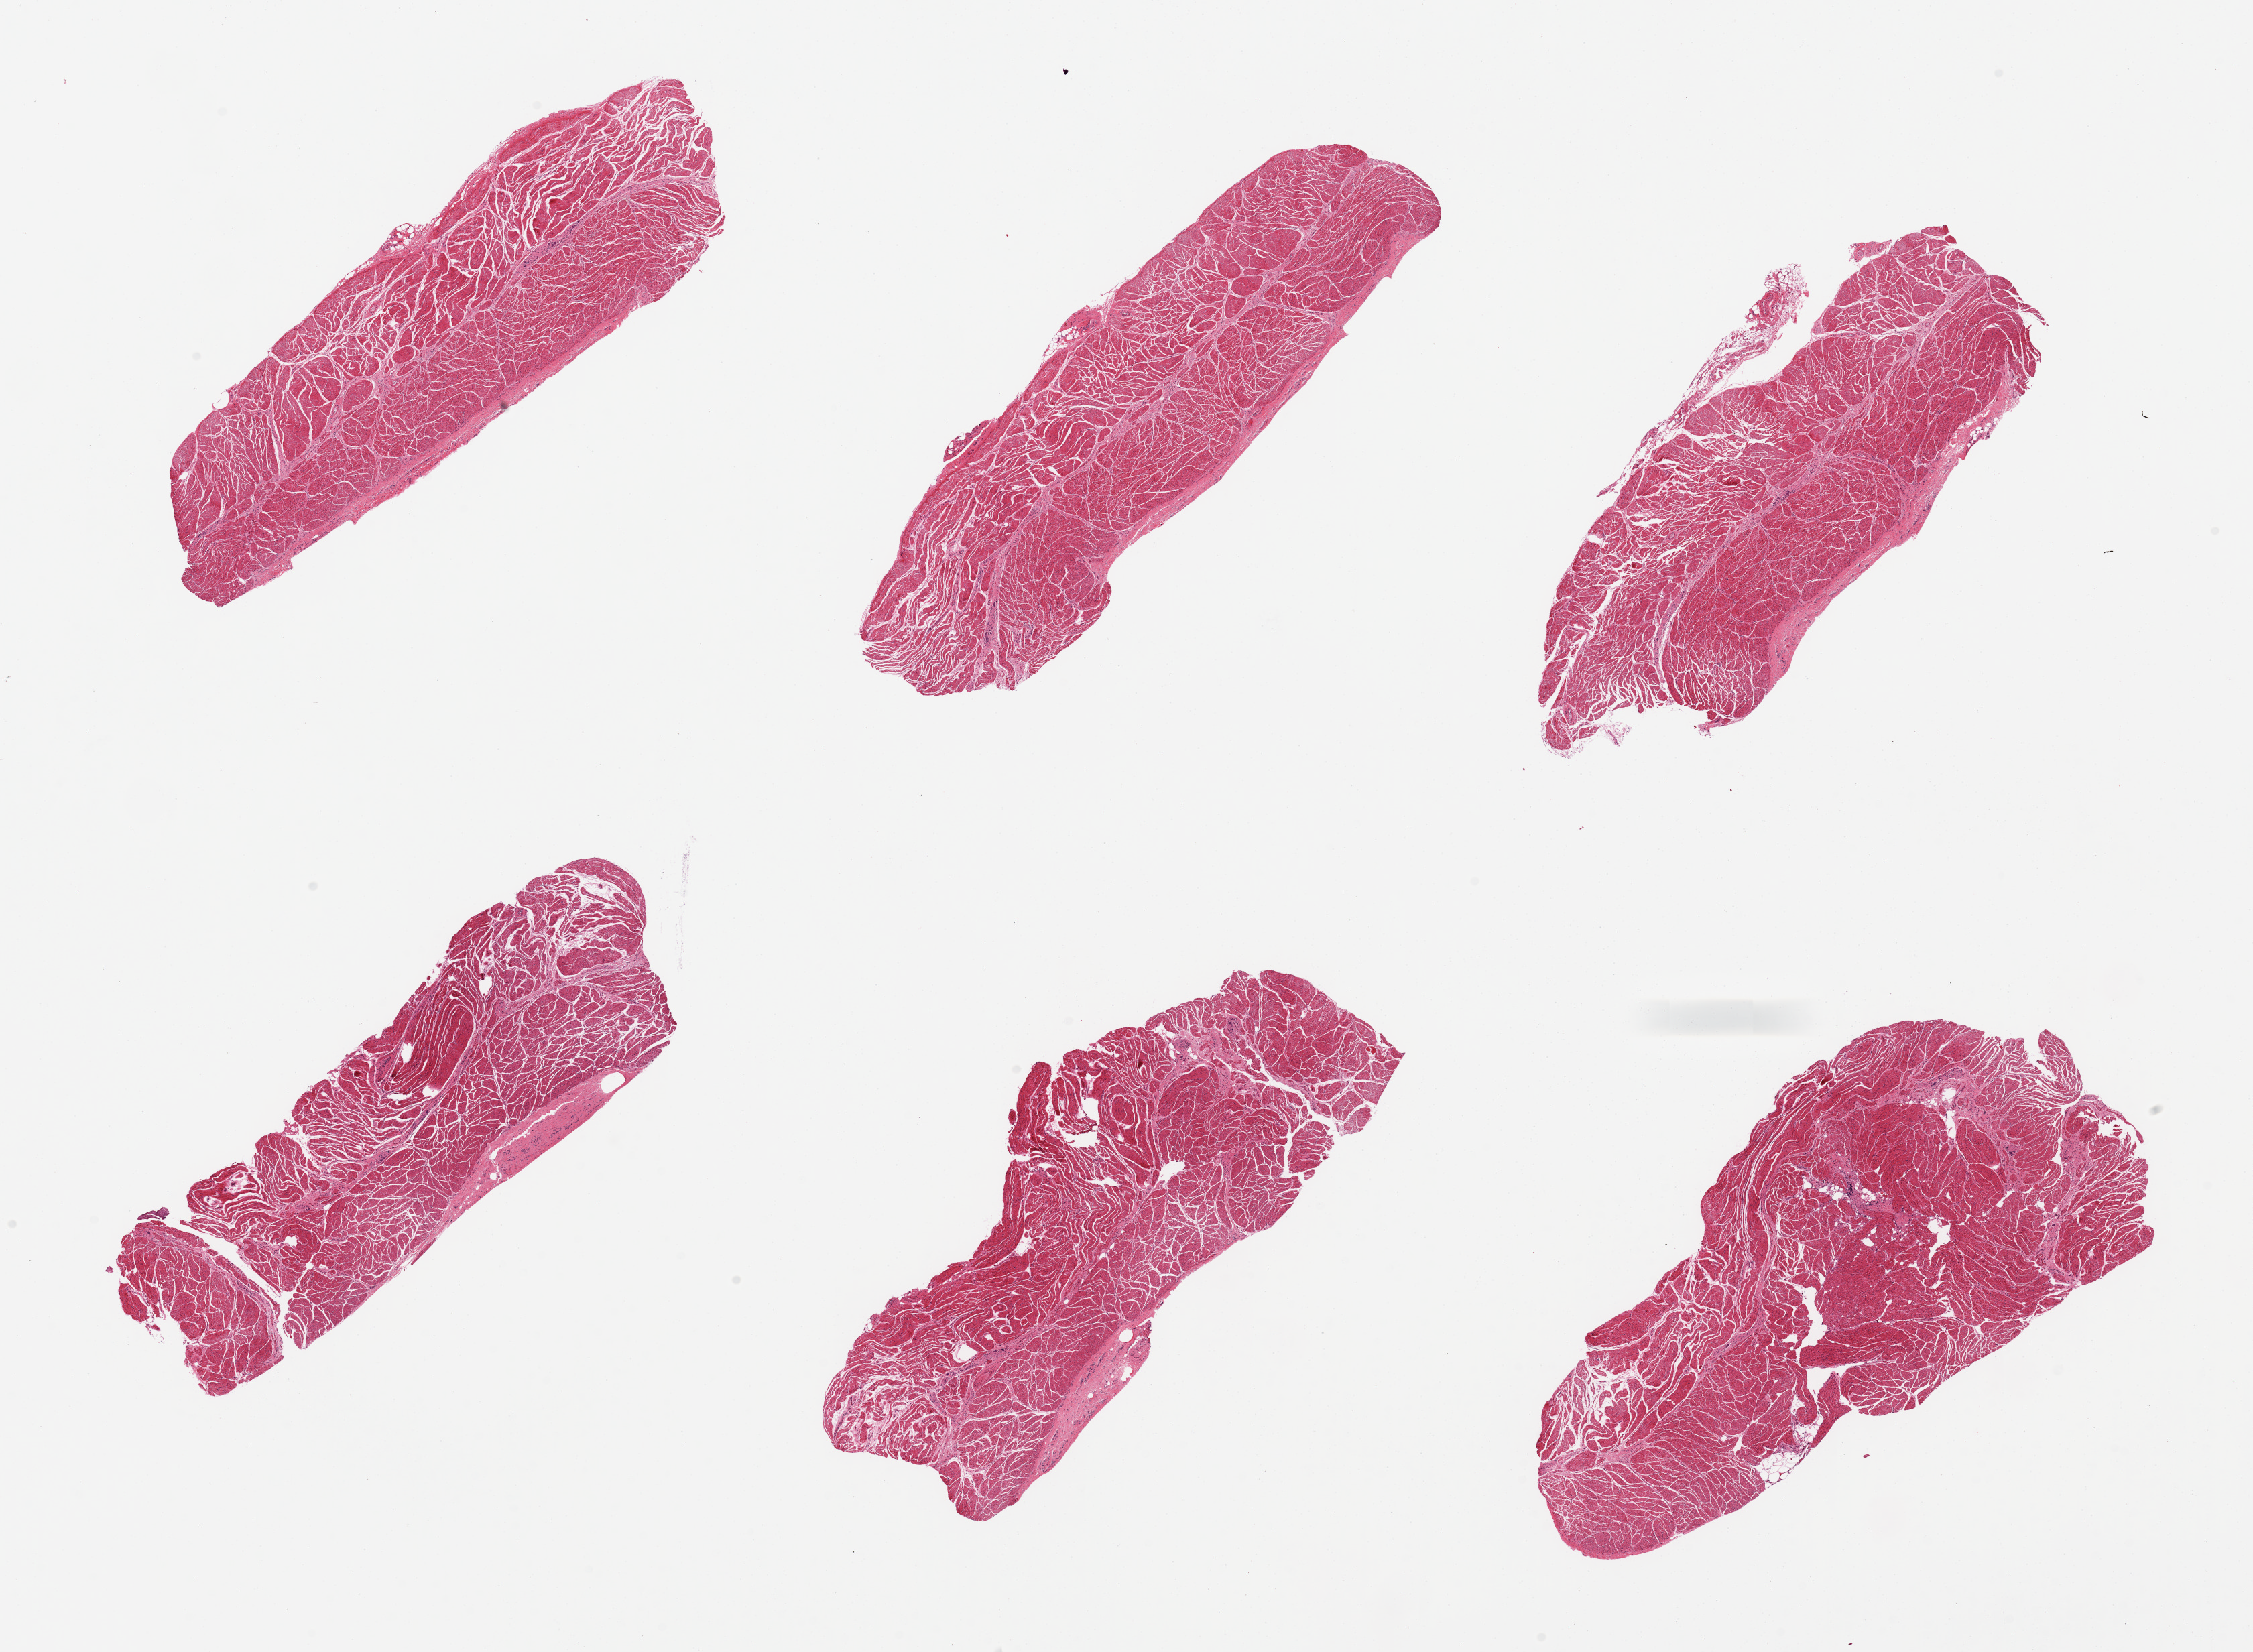
Digitized hematoxylin and eosin (H&E)-stained section — low-resolution overview of the scanned area, about 26.6 x 19.5 mm; PAXgene-fixed, paraffin-embedded tissue; sampled site (target tissue): esophageal muscle; donor tissue sample. Male donor.
Reviewer comment on this tissue sample: 6 pieces, well trimmed, small detached strip of squamous mucosa.